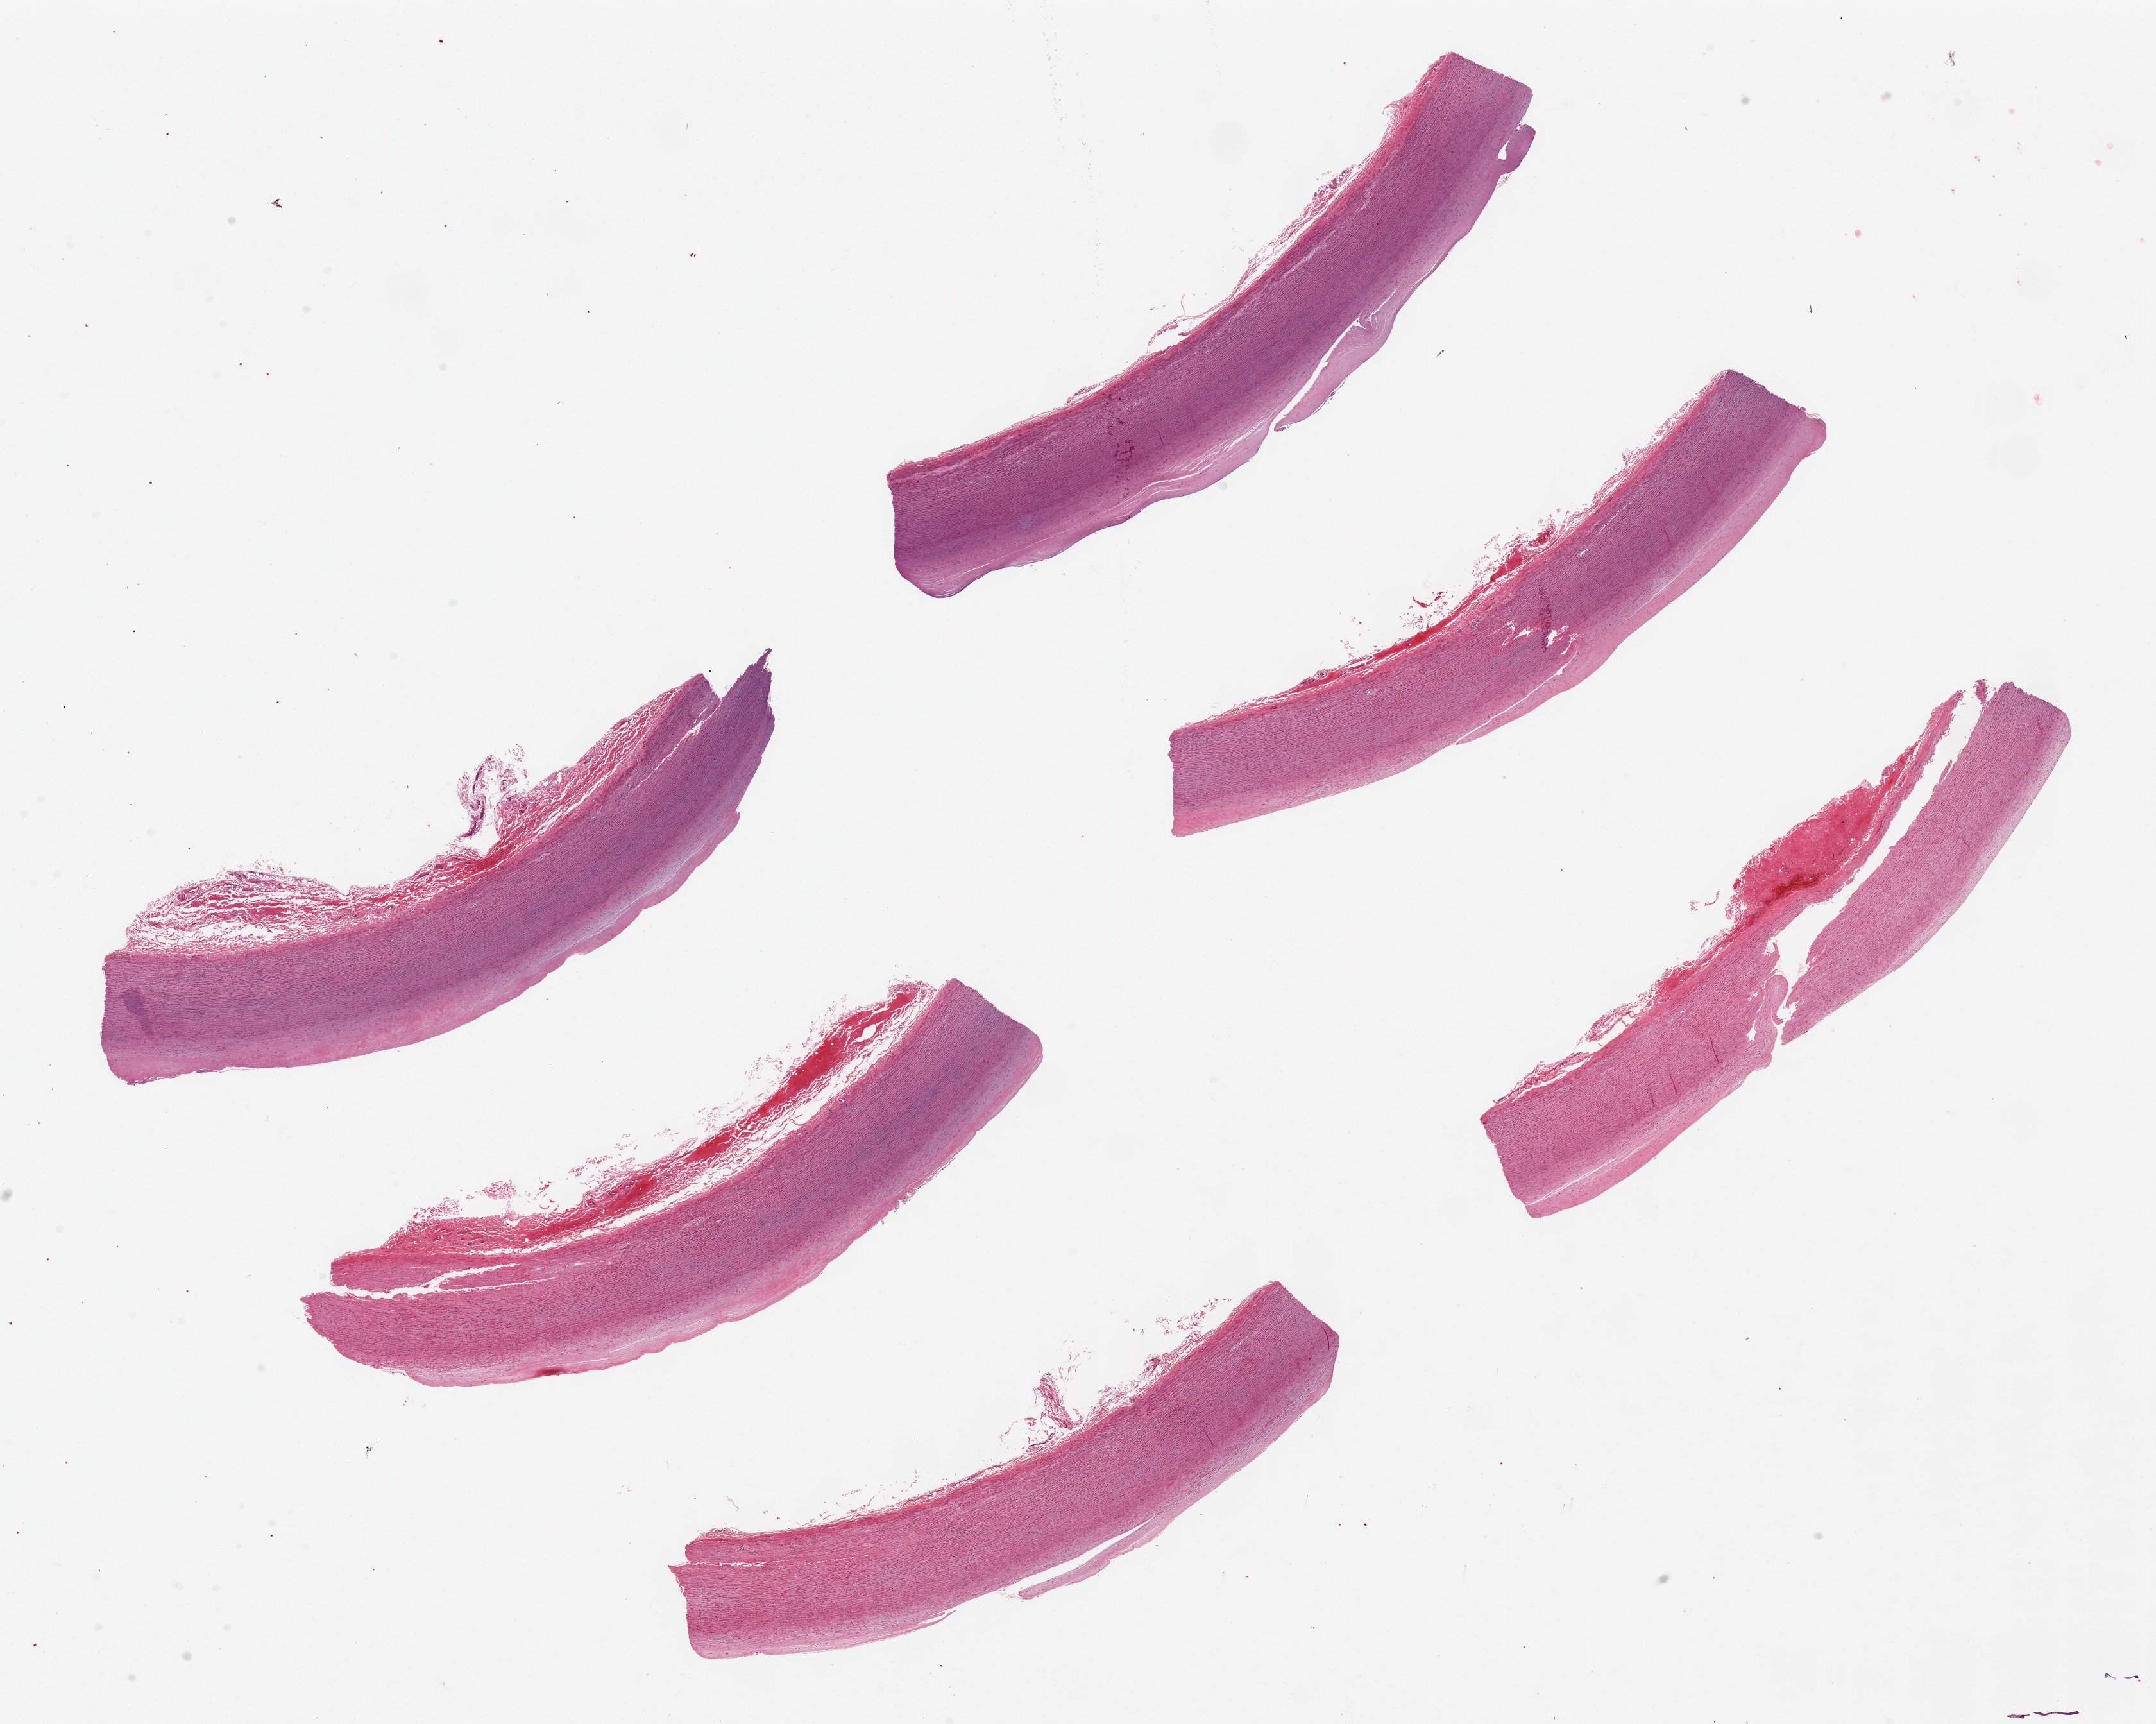
Digitized hematoxylin and eosin (H&E)-stained section, brightfield — a low-resolution overview of the entire scanned area, about 26.6 x 21.2 mm (acquisition: 20x scan), PAXgene-fixed, paraffin-embedded tissue, target tissue: aorta, donor tissue sample. Donor: male.
* review note (as recorded): 6 ~9x1.5mm pieces. Minimal atherosis